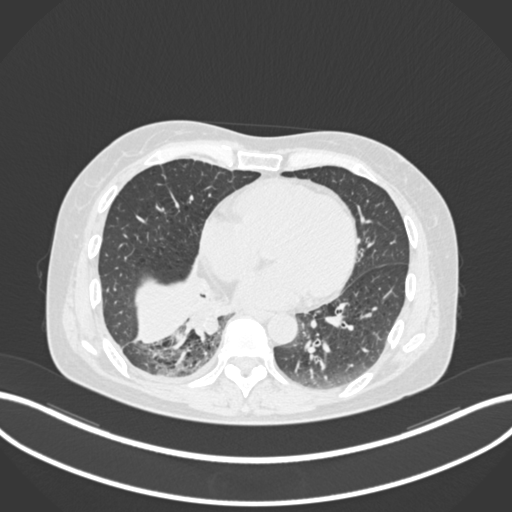
Chest CT, one axial slice. Slice 57 of 168 in the series (ordered by position). Lung window (W 1500 / L -600 HU). 512 × 512 image matrix. Patient: female, 63 years. Case-level facts recorded for this patient, not image findings: clinical TNM (as recorded): T1c N0 M0.
Annotated regions visible in this slice (bounding box drawn by a radiologist):
- lung tumour (recorded histology: adenocarcinoma): bounding box (x1, y1, x2, y2) in pixels: (186, 302, 228, 339)